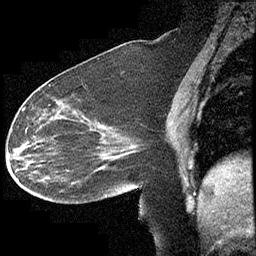
Breast MRI (dynamic contrast-enhanced), one sagittal slice; slice 164 of 232 in the series (ordered by position); dynamic contrast-enhanced study with each time point stored as its own series, time point 2 of 4 at this slice position (early post-contrast, ordered by acquisition time); 1.5 T; TE 4.2 ms, TR 6.7 ms; 3 mm slice thickness; 256 × 256 image matrix, field of view 200 × 200 mm. Patient: female, 63 years. From the clinical record (not read from this slice): setting: breast cancer imaged before/during neoadjuvant chemotherapy; receptor status: triple-negative.
Outlined on this slice (semi-automatic segmentation, software-assisted and operator-edited):
- analysis volume of interest (the breast-tissue region the enhancement analysis was run in; not a lesion): bounding box (x1, y1, x2, y2) in pixels: (13, 90, 140, 210)
- tumour enhancement mask (voxels above the 70 % enhancement threshold inside the analysis volume of interest): (23, 107, 100, 169)